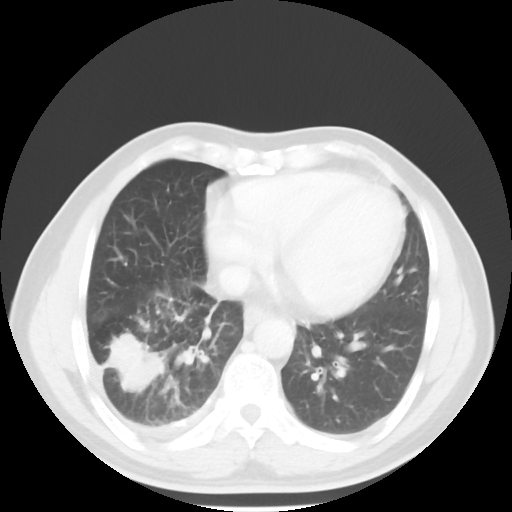
Chest CT, one axial slice. Position 20 of 56 along the scan axis. Lung window (W 1500 / L -600 HU). 5 mm slice thickness. 512 × 512 image matrix. Patient: male, 56 years. Case-level facts recorded for this patient, not image findings: clinical TNM (as recorded): T2 N3 M1.
Structures marked on this image (bounding box drawn by a radiologist):
- lung tumour (recorded histology: adenocarcinoma): bounding box (x1, y1, x2, y2) in pixels: (104, 332, 166, 397)